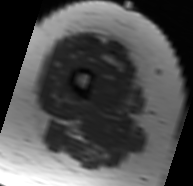
MRI of an extremity soft-tissue mass, one axial slice; slice 13 of 91 in the series (ordered by position); MR volume resampled by the dataset authors to the PET/CT grid (not the native acquisition matrix); 193 × 186 image matrix, field of view 188 × 182 mm. Female patient. Case-level facts recorded for this patient, not image findings: histological type: malignant solitary fibrous tumor; grade: intermediate; site of the primary tumour: right thigh.
Structures marked on this image (expert contour drawn on MRI and transferred to this co-registered scan by the dataset authors):
- gross tumour volume including surrounding oedema: bounding box <74,37,125,70> (left, top, right, bottom; pixels)